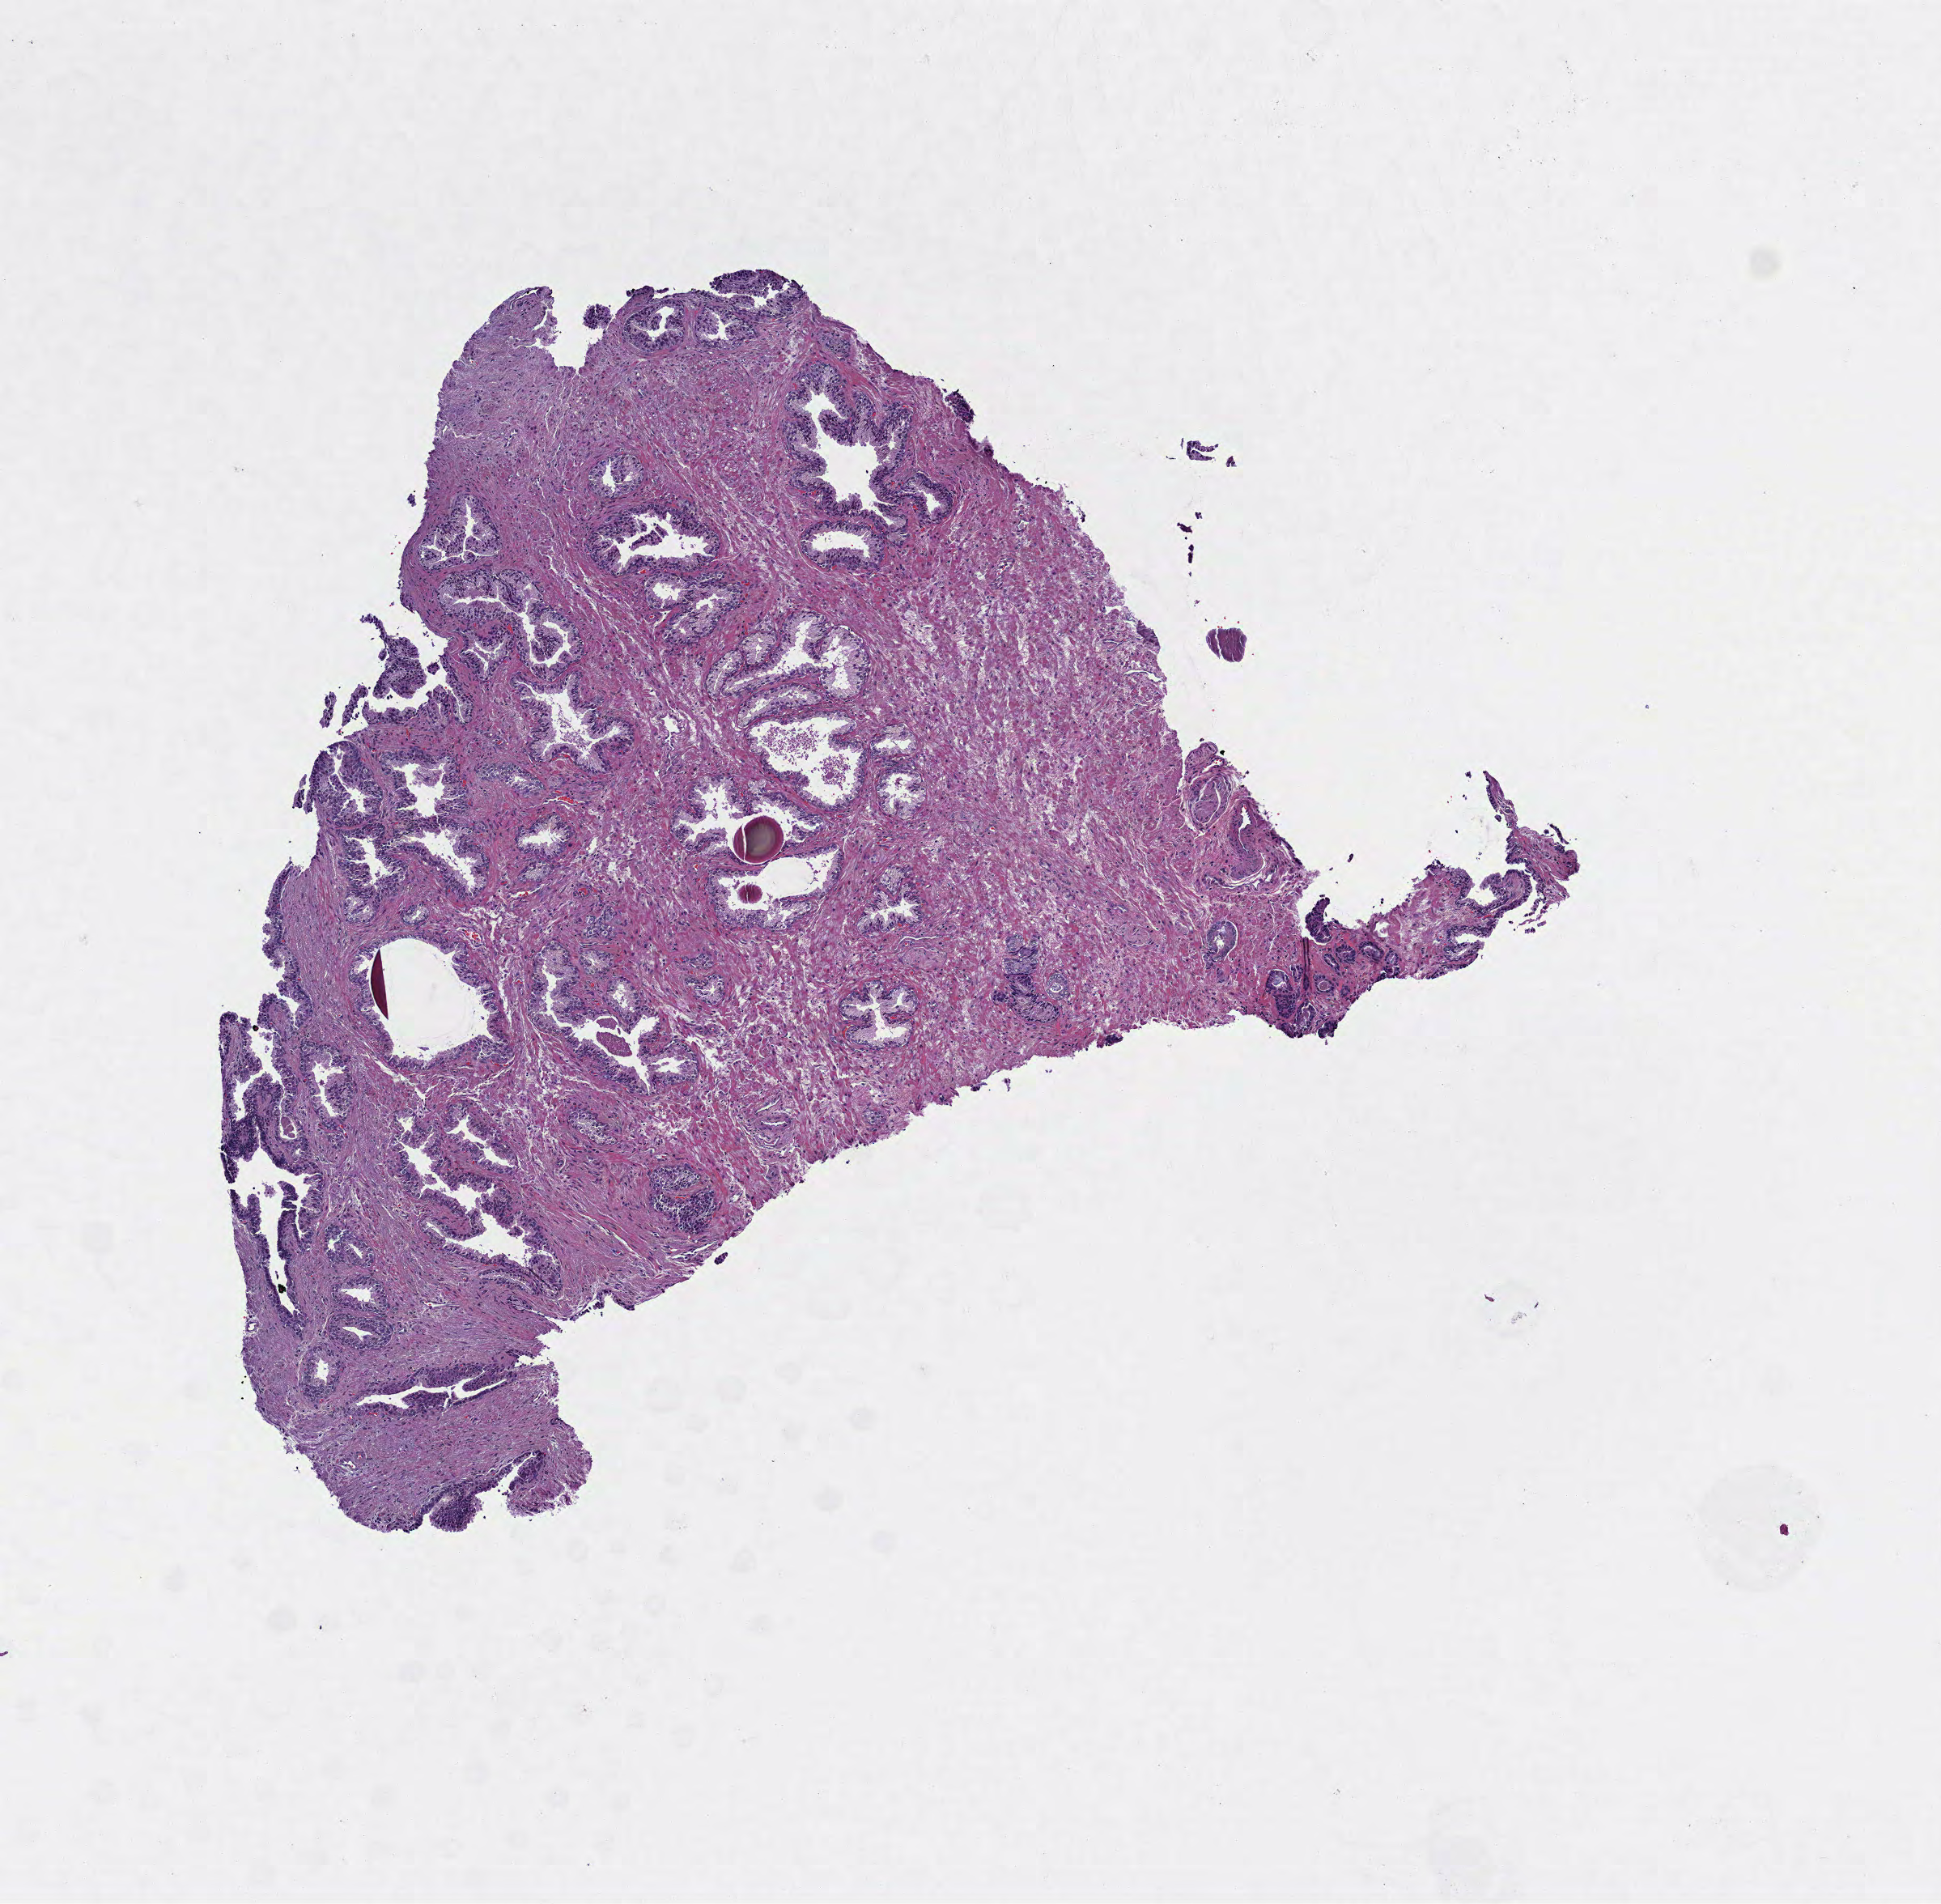
Whole-slide histology image, H&E-stained — whole scanned area (about 4.8 x 4.7 mm) shown as a low-resolution overview, FFPE section, primary tumour sample from the prostate. Patient: male, age at initial diagnosis 51 years. Gleason score: 7 (3+4).
Histologic diagnosis: Adenocarcinoma, NOS (prostate gland).